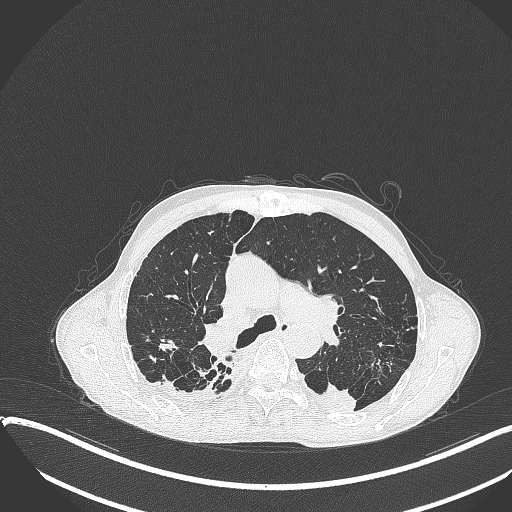
Chest CT, one axial slice. Slice 257 of 401 in the series (ordered by position). 120 kVp. Lung window (W 1500 / L -600 HU). 1 mm slice thickness. 512 × 512 image matrix, field of view 400 × 400 mm. Patient: male, 57 years. From the clinical record (not read from this slice): clinical TNM (as recorded): T4 N0 M0.
Outlined on this slice (rectangle marked by the reading radiologist):
- lung tumour (recorded histology: squamous cell carcinoma): box from (x=302, y=376) to (x=358, y=418) px